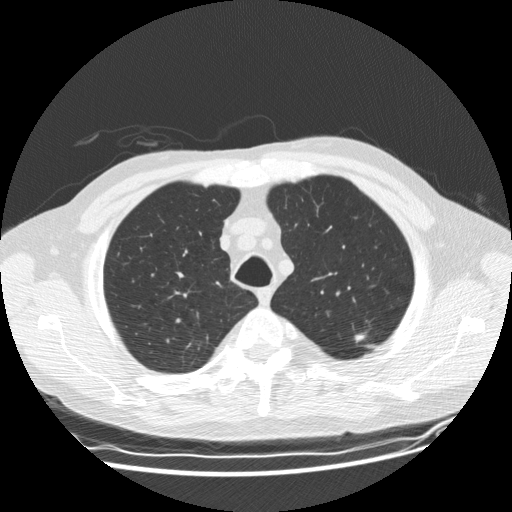
Low-dose screening chest CT, one axial slice; slice 147 of 177 in the series (ordered by position); reconstruction kernel STANDARD; 120 kVp; lung window (W 1500 / L -600 HU); 2.5 mm slice thickness; 512 × 512 image matrix, field of view 360 × 360 mm.
Annotated regions visible in this slice (outlined manually by an expert reader):
- lesion 1 (tumor, upper lobe of left lung): bounding box (x1, y1, x2, y2) in pixels: (355, 332, 366, 343)